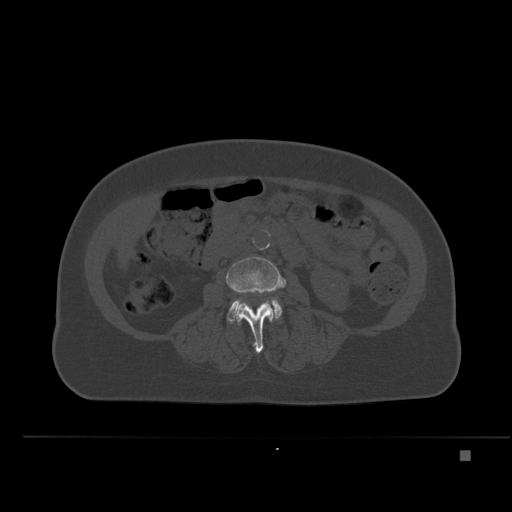
CT including the spine, one axial slice. Slice 192 of 477 in the series (ordered by position). Bone window (W 1800 / L 400 HU). 1.5 mm slice thickness. 512 × 512 image matrix, field of view 422 × 422 mm. Patient: female, 74 years. From the clinical record (not read from this slice): primary cancer: colon.
Structures marked on this image (semi-automatically segmented with operator editing):
- L3 vertebra: bounding box <226,257,286,353> (left, top, right, bottom; pixels)
- L4 vertebra: <227,298,282,322>